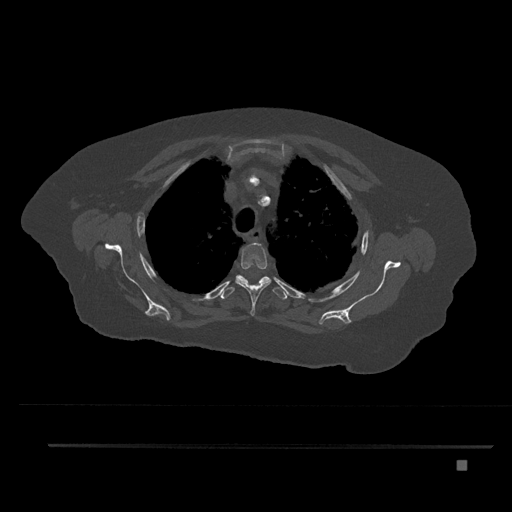
CT including the spine, one axial slice; position 626 of 797 along the scan axis; 120 kVp; bone window (W 1800 / L 400 HU); 512 × 512 image matrix, field of view 437 × 437 mm. Patient: female, 76 years. From the clinical record (not read from this slice): primary cancer: lung.
Outlined on this slice (semi-automatic segmentation, software-assisted and operator-edited):
- T3 vertebra: bounding box [x1, y1, x2, y2] px = [235, 243, 271, 316]
- T4 vertebra: [220, 275, 287, 300]